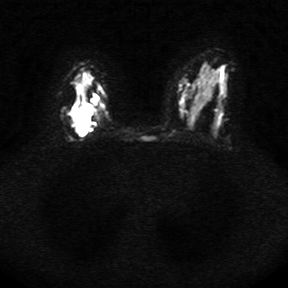
Breast MRI, one axial slice; position 18 of 34 along the scan axis; diffusion-weighted series; image 2 of 4 stored at this slice position (different b-values; order by instance number); 1.5 T; 5 mm slice thickness; 288 × 288 image matrix, field of view 340 × 340 mm. Female patient.
Structures marked on this image (manually delineated by an expert):
- tumour on diffusion-weighted imaging: bounding box (x1, y1, x2, y2) in pixels: (70, 103, 92, 135)